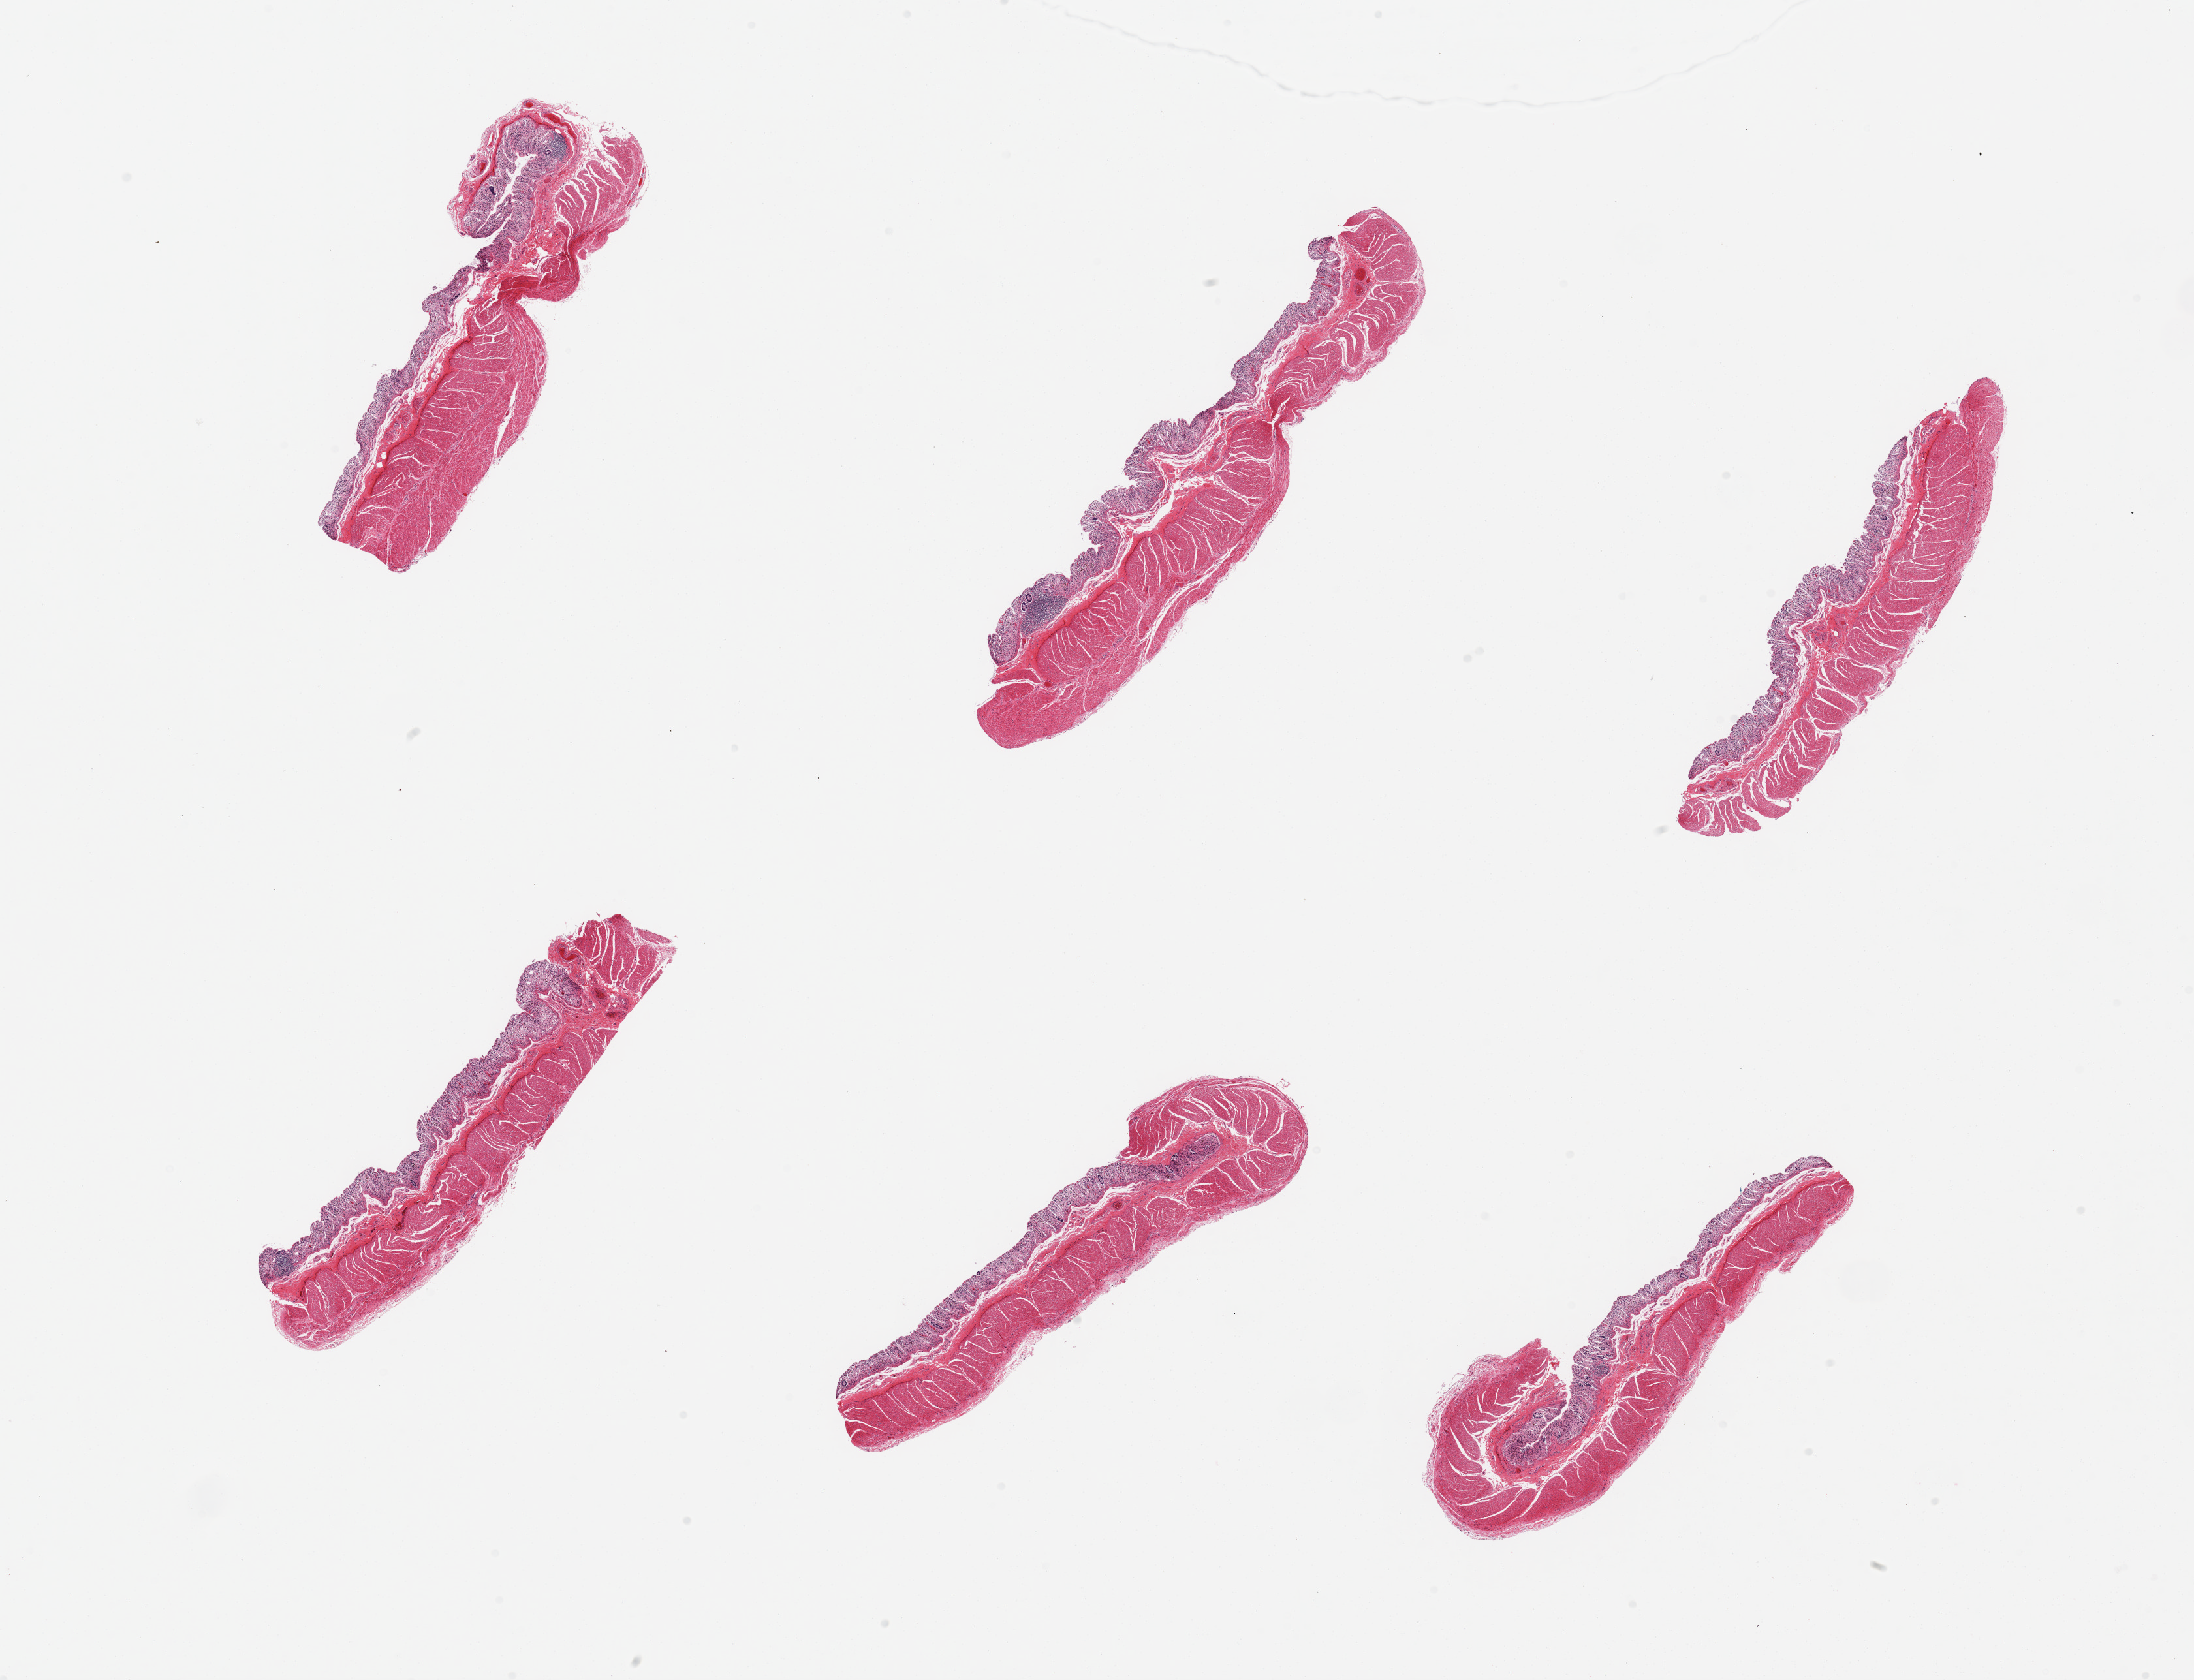
Haematoxylin and eosin whole-slide image, whole scanned area (about 26.6 x 20.4 mm, from a 20x scan) shown as a low-resolution overview, PAXgene-fixed, paraffin-embedded tissue, sampled site (target tissue): transverse colon, donor tissue sample. Female donor.
Pathologist's review note for this sample: 6 pieces; mucosal glands autolyzed; muscle preserved; well trimmed.